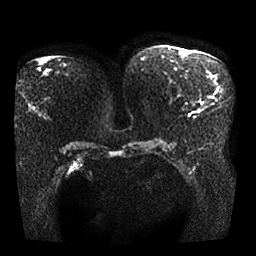
Breast MRI, one axial slice. Position 7 of 25 along the scan axis. Diffusion-weighted series; image 2 of 4 stored at this slice position (different b-values; order by instance number). 1.5 T. 4 mm slice thickness. 256 × 256 image matrix, field of view 370 × 370 mm. Female patient.
Structures marked on this image (expert manual segmentation):
- tumour on diffusion-weighted imaging: bounding box <199,107,207,111> (left, top, right, bottom; pixels)